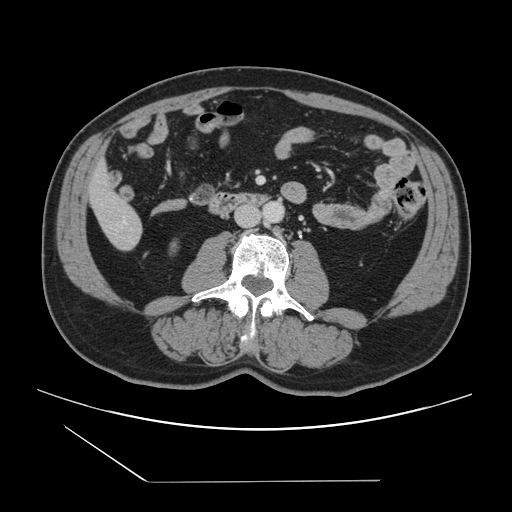
Contrast-enhanced abdominal CT, one axial slice; slice 22 of 157 in the series (ordered by position); intravenous contrast given; soft-tissue window (W 400 / L 40 HU); 2.5 mm slice thickness; 512 × 512 image matrix, field of view 407 × 407 mm. Male patient, age 61 years. Case-level facts recorded for this patient, not image findings: diagnosis: colorectal cancer liver metastases, imaged before liver resection; multiple liver metastases: yes; largest metastasis: 5.5 cm.
Outlined on this slice (manually delineated by an expert):
- liver: bounding box (x1, y1, x2, y2) in pixels: (91, 166, 142, 250)
- planned liver remnant (the part of the liver to remain after resection): (91, 165, 131, 218)